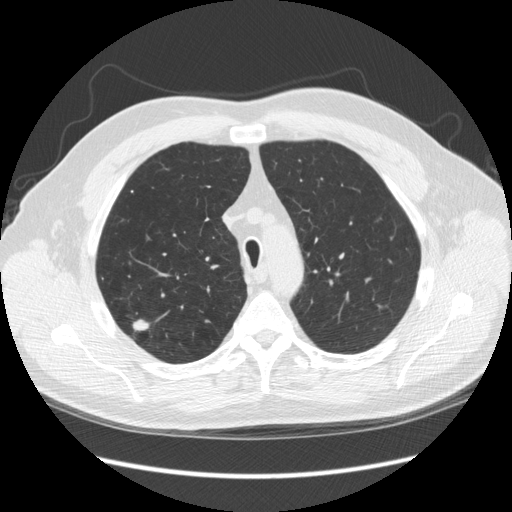
Low-dose screening chest CT, one axial slice; slice 191 of 248 in the series (ordered by position); lung window (W 1500 / L -600 HU); 2.5 mm slice thickness; 512 × 512 image matrix, field of view 380 × 380 mm.
Annotated regions visible in this slice (outlined manually by an expert reader):
- lesion 1 (tumor, upper lobe of right lung): bounding box <133,319,149,331> (left, top, right, bottom; pixels)